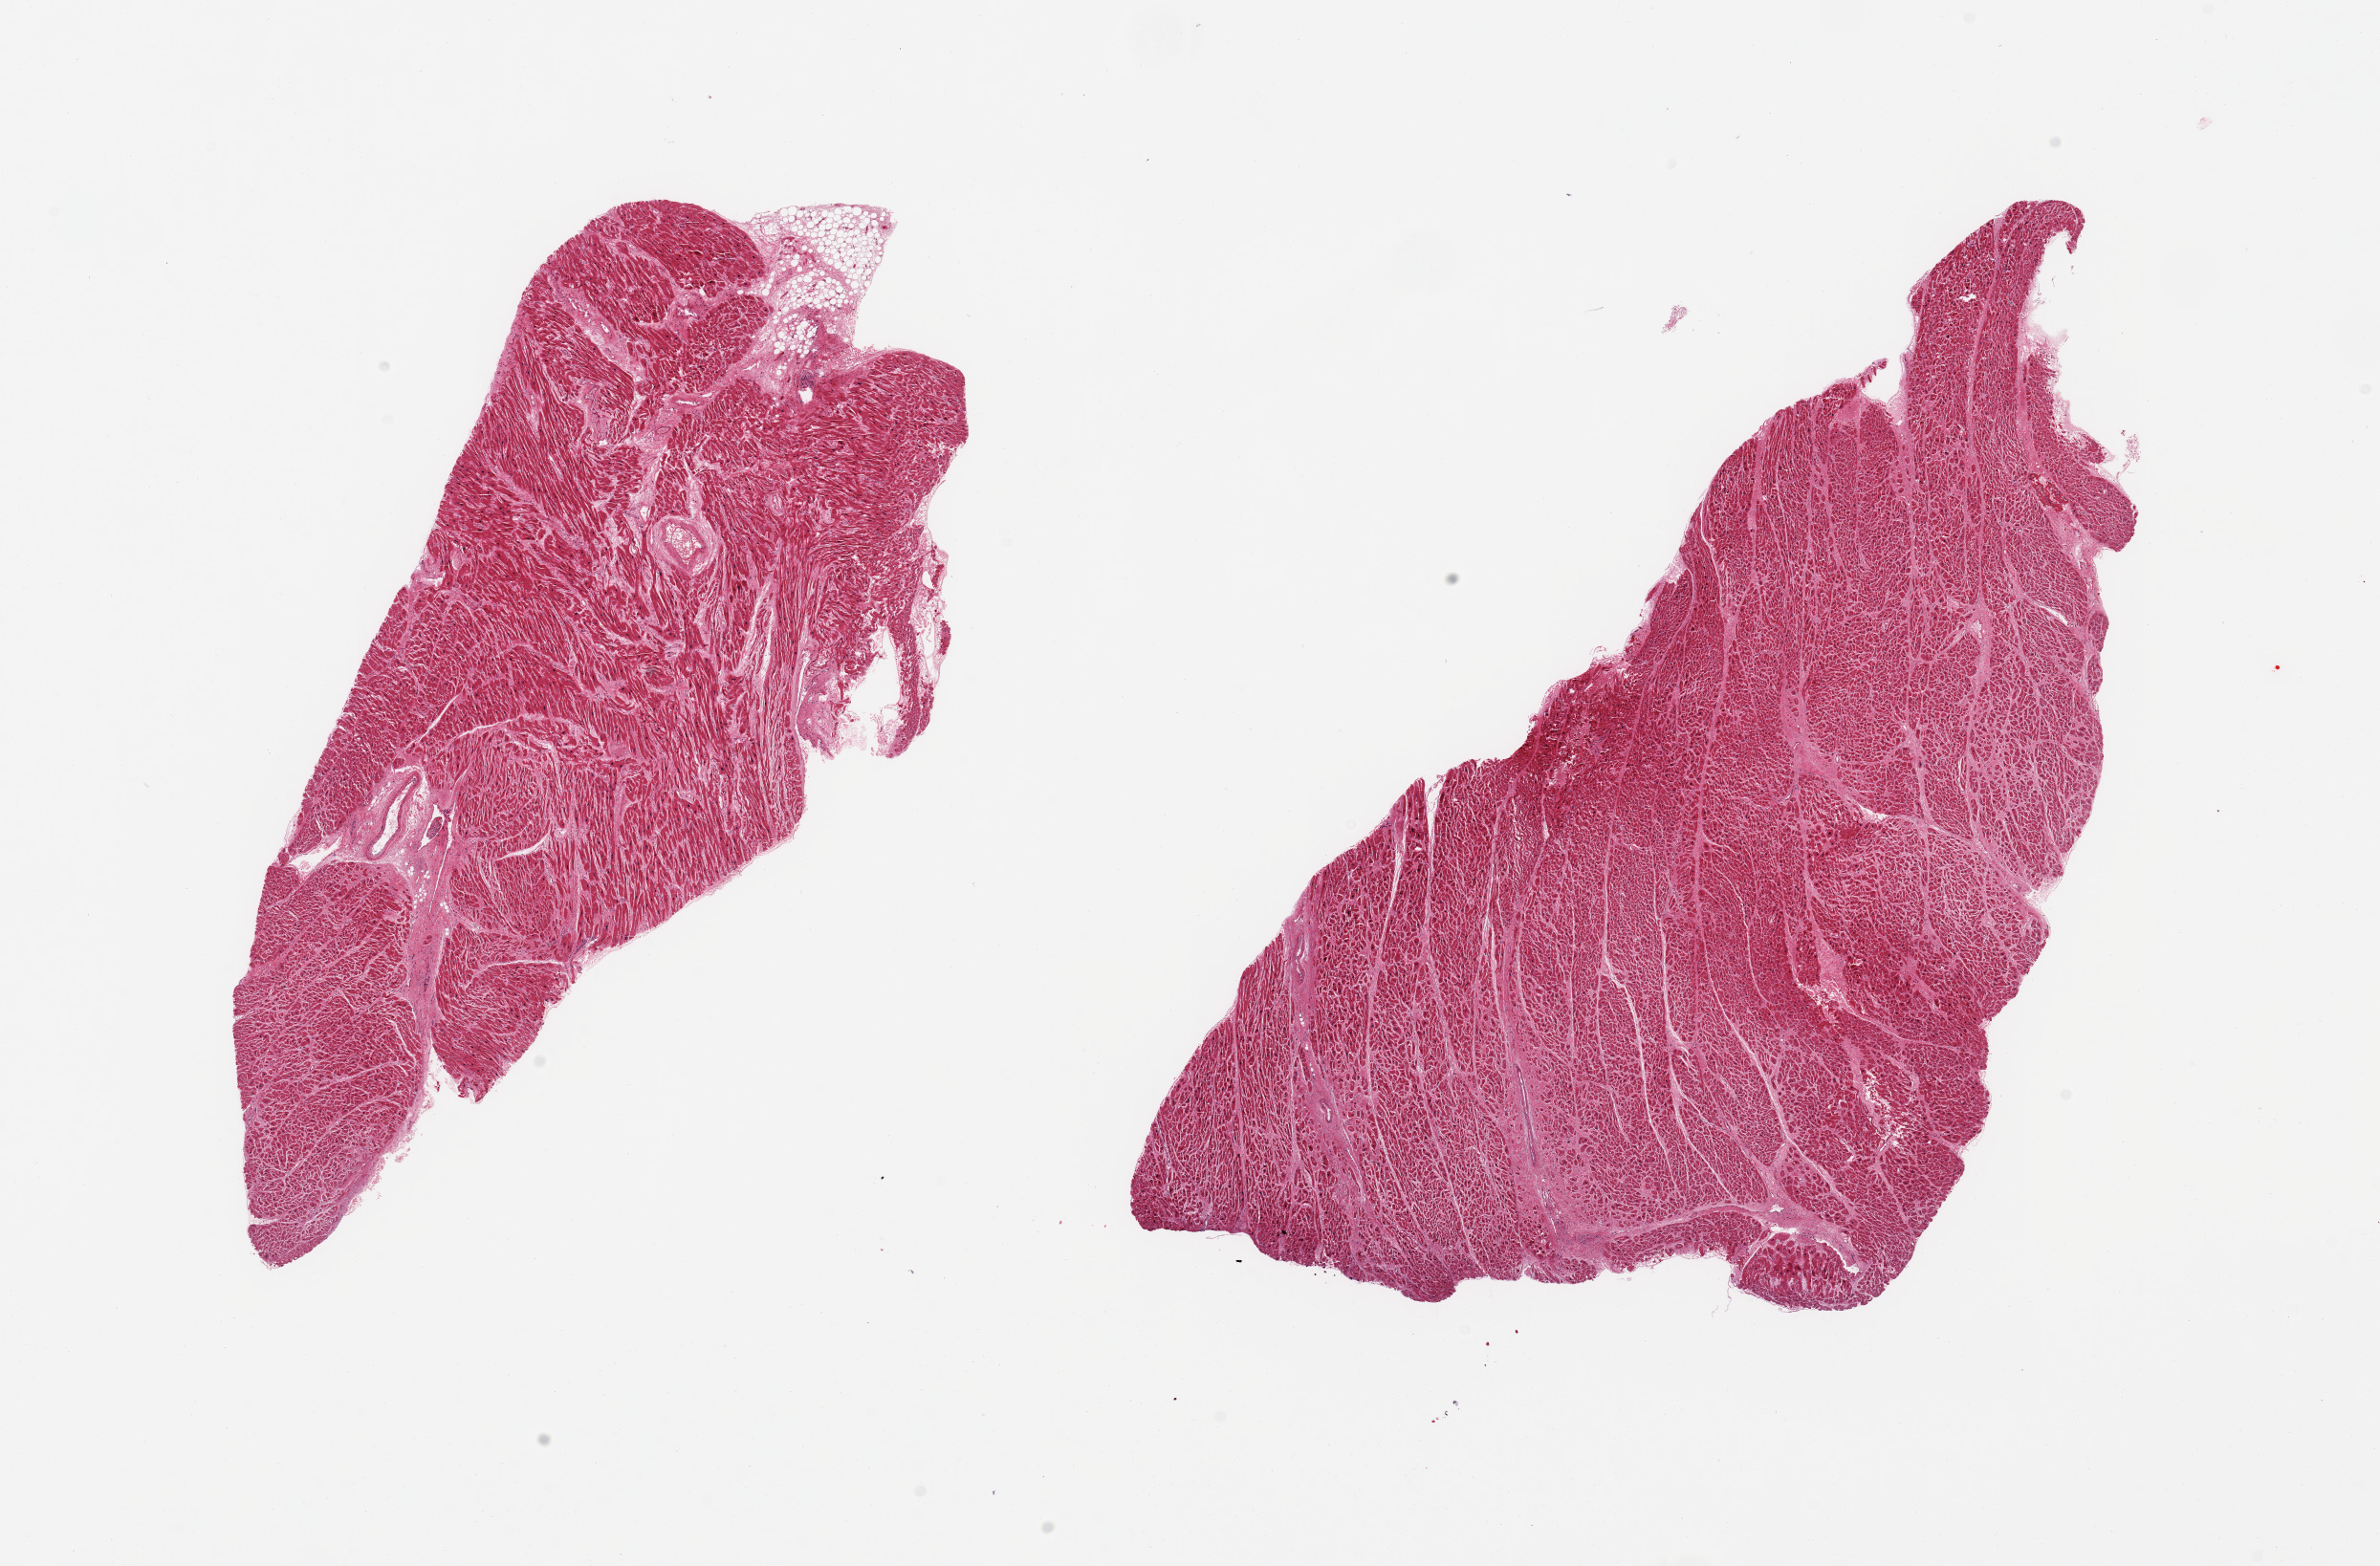
Whole-slide image, H&E stain — low-resolution overview of the scanned area, about 19.7 x 13.0 mm (slide scanned at 20x); PAXgene-fixed paraffin-embedded (PFPE) section; sampled site (target tissue): heart; donor tissue sample.
• reviewer comment on this tissue sample: 2 pieces, patchy severe interstitial fibrosis/choronic sichemic changes, remote micro infarcts